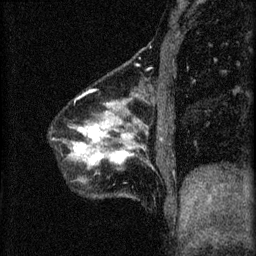
Breast MRI (dynamic contrast-enhanced), one sagittal slice. Slice 13 of 60 in the series (ordered by position). 3 images stored at this slice position (order not interpretable as contrast timing). 1.5 T. TE 4.2 ms, TR 8.2 ms. 256 × 256 image matrix, field of view 180 × 180 mm. Patient: female, 40 years.
Structures marked on this image (semi-automatic segmentation, software-assisted and operator-edited):
- analysis volume of interest (the breast-tissue region the enhancement analysis was run in; not a lesion): bounding box (x1, y1, x2, y2) in pixels: (68, 92, 163, 199)
- tumour enhancement mask (voxels above the 70 % enhancement threshold inside the analysis volume of interest): (74, 126, 131, 165)